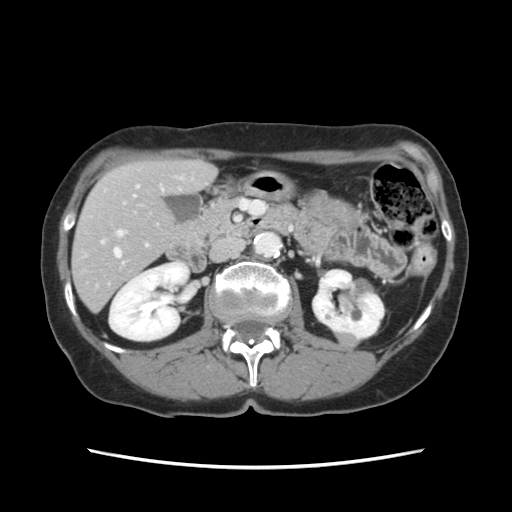
Contrast-enhanced abdominal CT, one axial slice; slice 52 of 120 in the series (ordered by position); 120 kVp; intravenous contrast given; soft-tissue window (W 400 / L 40 HU); 2.5 mm slice thickness; 512 × 512 image matrix. Female patient, age 70 years. From the clinical record (not read from this slice): diagnosis: colorectal cancer liver metastases, imaged before liver resection; multiple liver metastases: no; largest metastasis: 2.5 cm; disease in both lobes: no.
Outlined on this slice (expert manual segmentation):
- hepatic veins: box from (x=114, y=249) to (x=121, y=257) px
- liver: (x=73, y=161)–(x=215, y=310)
- planned liver remnant (the part of the liver to remain after resection): (x=73, y=161)–(x=215, y=309)
- portal vein (with intrahepatic branches): (x=101, y=178)–(x=182, y=247)